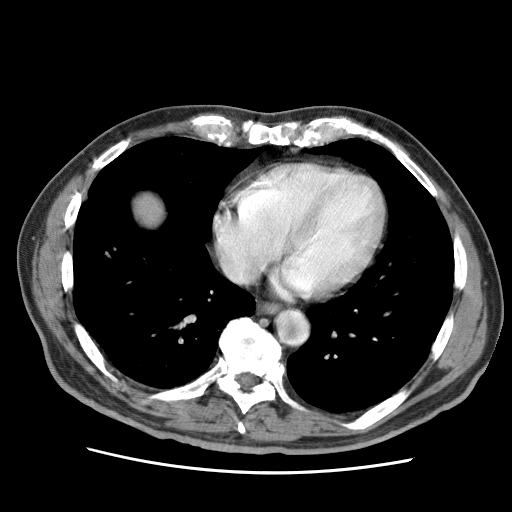
Contrast-enhanced abdominal CT (liver protocol), one axial slice. Position 69 of 75 along the scan axis. Reconstruction kernel STANDARD. 120 kVp. Soft-tissue window (W 400 / L 40 HU). 2.5 mm slice thickness. 512 × 512 image matrix, field of view 360 × 360 mm. From the clinical record (not read from this slice): diagnosis: hepatocellular carcinoma (patient treated with transarterial chemoembolisation; whether this scan precedes or follows treatment is not stated here); TNM stage (as recorded): Stage-IIIA; Child-Pugh class: A; tumour differentiation: well differentiated; tumour nodularity: multinodular.
Annotated regions visible in this slice (semi-automatic segmentation, software-assisted and operator-edited):
- liver parenchyma outside the tumour (the mass and vessels are separate outlines, so this box may not span the whole liver): bounding box [x1, y1, x2, y2] px = [135, 194, 164, 225]